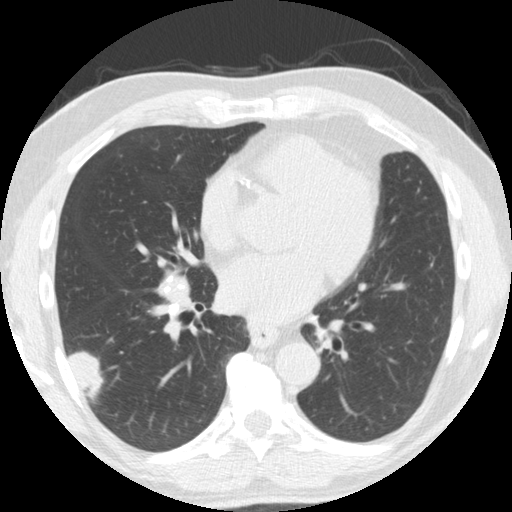
Axial slice from a low-dose chest CT screening exam; second annual screen; lung window (W 1500 / L -600 HU); standard (soft-tissue) reconstruction kernel (STANDARD); slice 96 of 174 in the series. Male, age 61 years at enrolment. Former smoker at enrolment.
• Lesion marked by an expert reader, bounding box <49,325,117,400> (left, top, right, bottom; pixels).
• Reader record for this screening exam (exam-level; its link to the box is not recorded): non-calcified nodule or mass ≥4 mm, right lower lobe, 33 × 19 mm, smooth margins, soft tissue attenuation, pre-existing on the prior screen: yes; interval growth: yes.
• Official screen result: positive, change unspecified: nodule(s) >= 4 mm or enlarging nodule(s), mass(es), or other non-specific abnormalities suspicious for lung cancer.
• Later outcome: lung cancer diagnosed 30 days after this screen — adenosquamous carcinoma, right lower lobe, poorly differentiated (G3), stage IV (AJCC 6th edition), 45 mm at pathology.